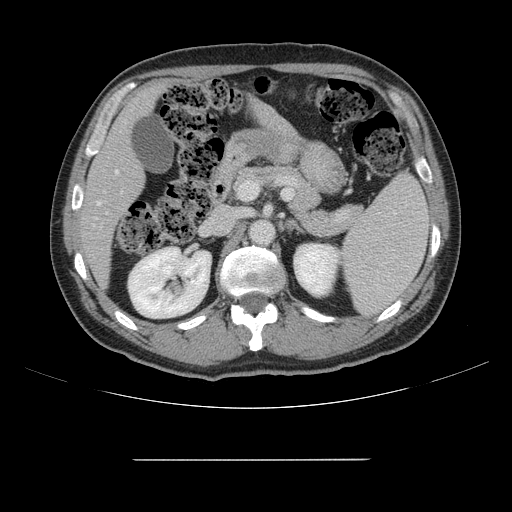
Contrast-enhanced abdominal CT, one axial slice. Soft-tissue window (W 400 / L 40 HU). 2.5 mm slice thickness. 512 × 512 image matrix, field of view 404 × 404 mm. Male patient, age 54 years. Case-level facts recorded for this patient, not image findings: diagnosis: colorectal cancer liver metastases, imaged before liver resection; multiple liver metastases: yes; largest metastasis: 1 cm; disease in both lobes: no.
Annotated regions visible in this slice (expert manual segmentation):
- hepatic veins: bounding box (x1, y1, x2, y2) in pixels: (97, 170, 119, 205)
- liver: (84, 89, 288, 282)
- planned liver remnant (the part of the liver to remain after resection): (84, 89, 157, 282)